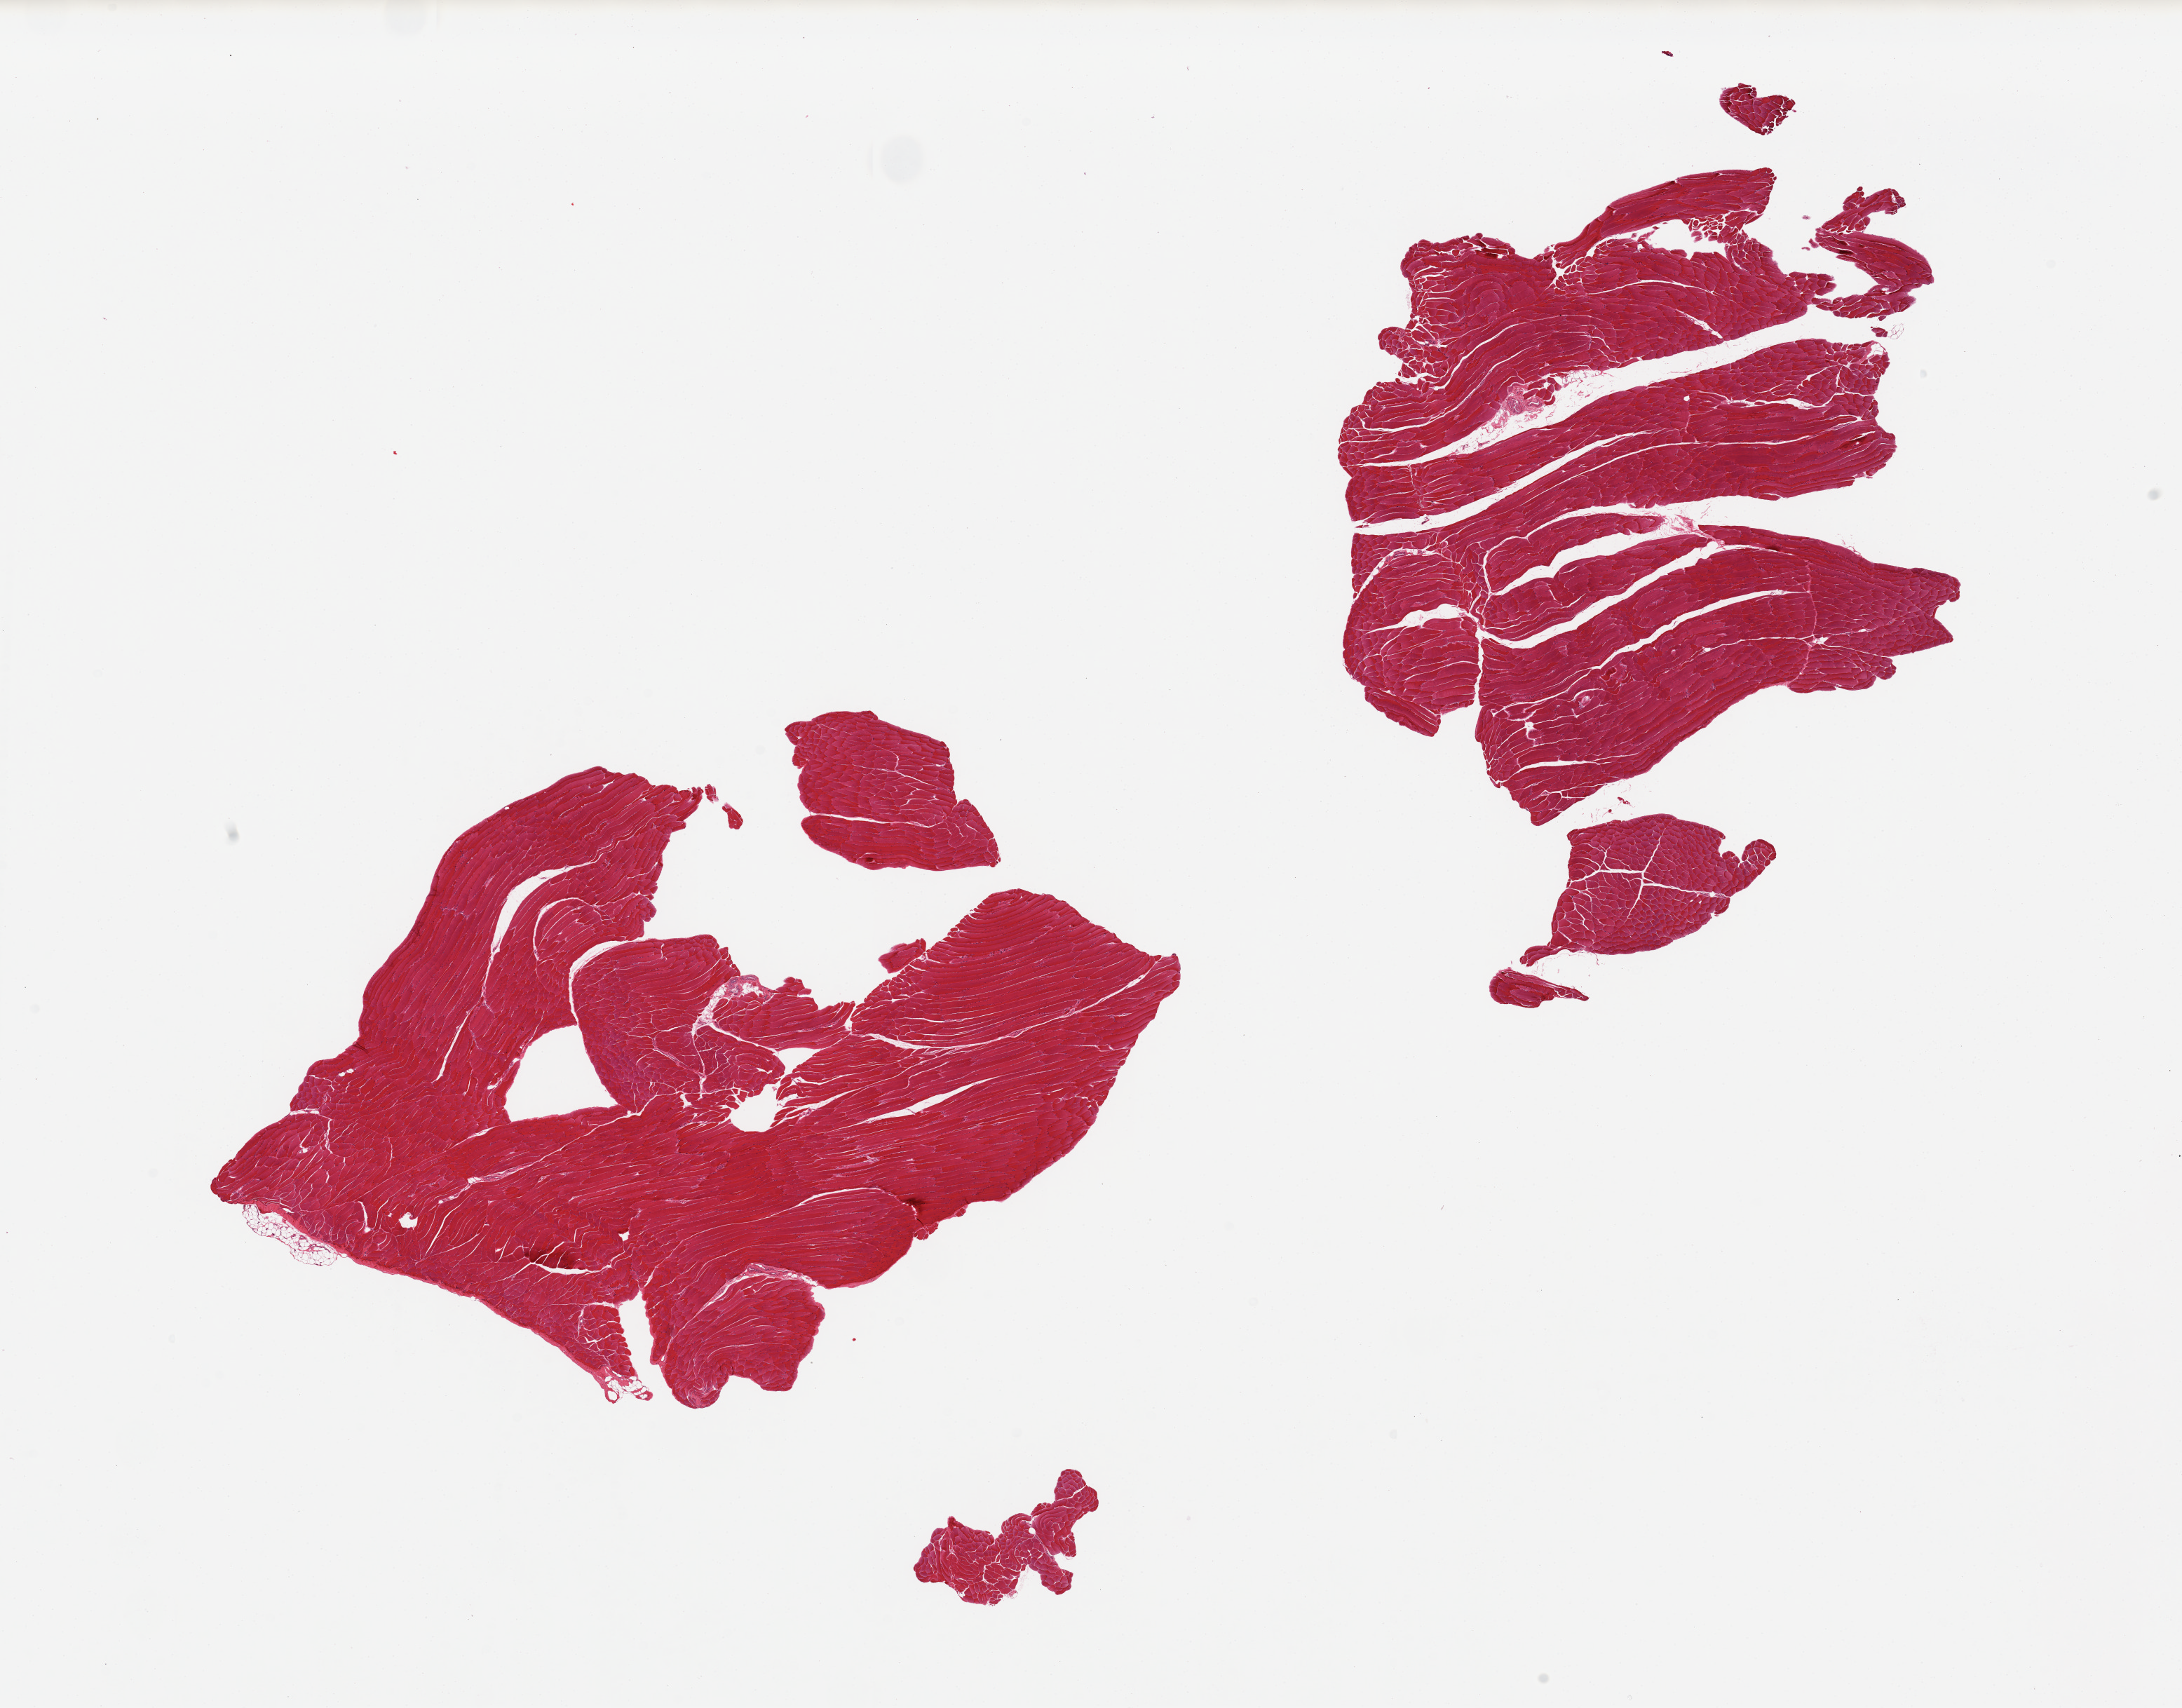
Digitized hematoxylin and eosin (H&E)-stained section, whole scanned area (about 24.6 x 19.3 mm, slide scanned at 20x) shown as a low-resolution overview. PAXgene-fixed paraffin-embedded (PFPE) section. Section of skeletal muscle (target tissue). Tissue donor sample. Donor sex: female.
Reviewer comment on this tissue sample: 2 pieces trace interstitial fat, good specimens.